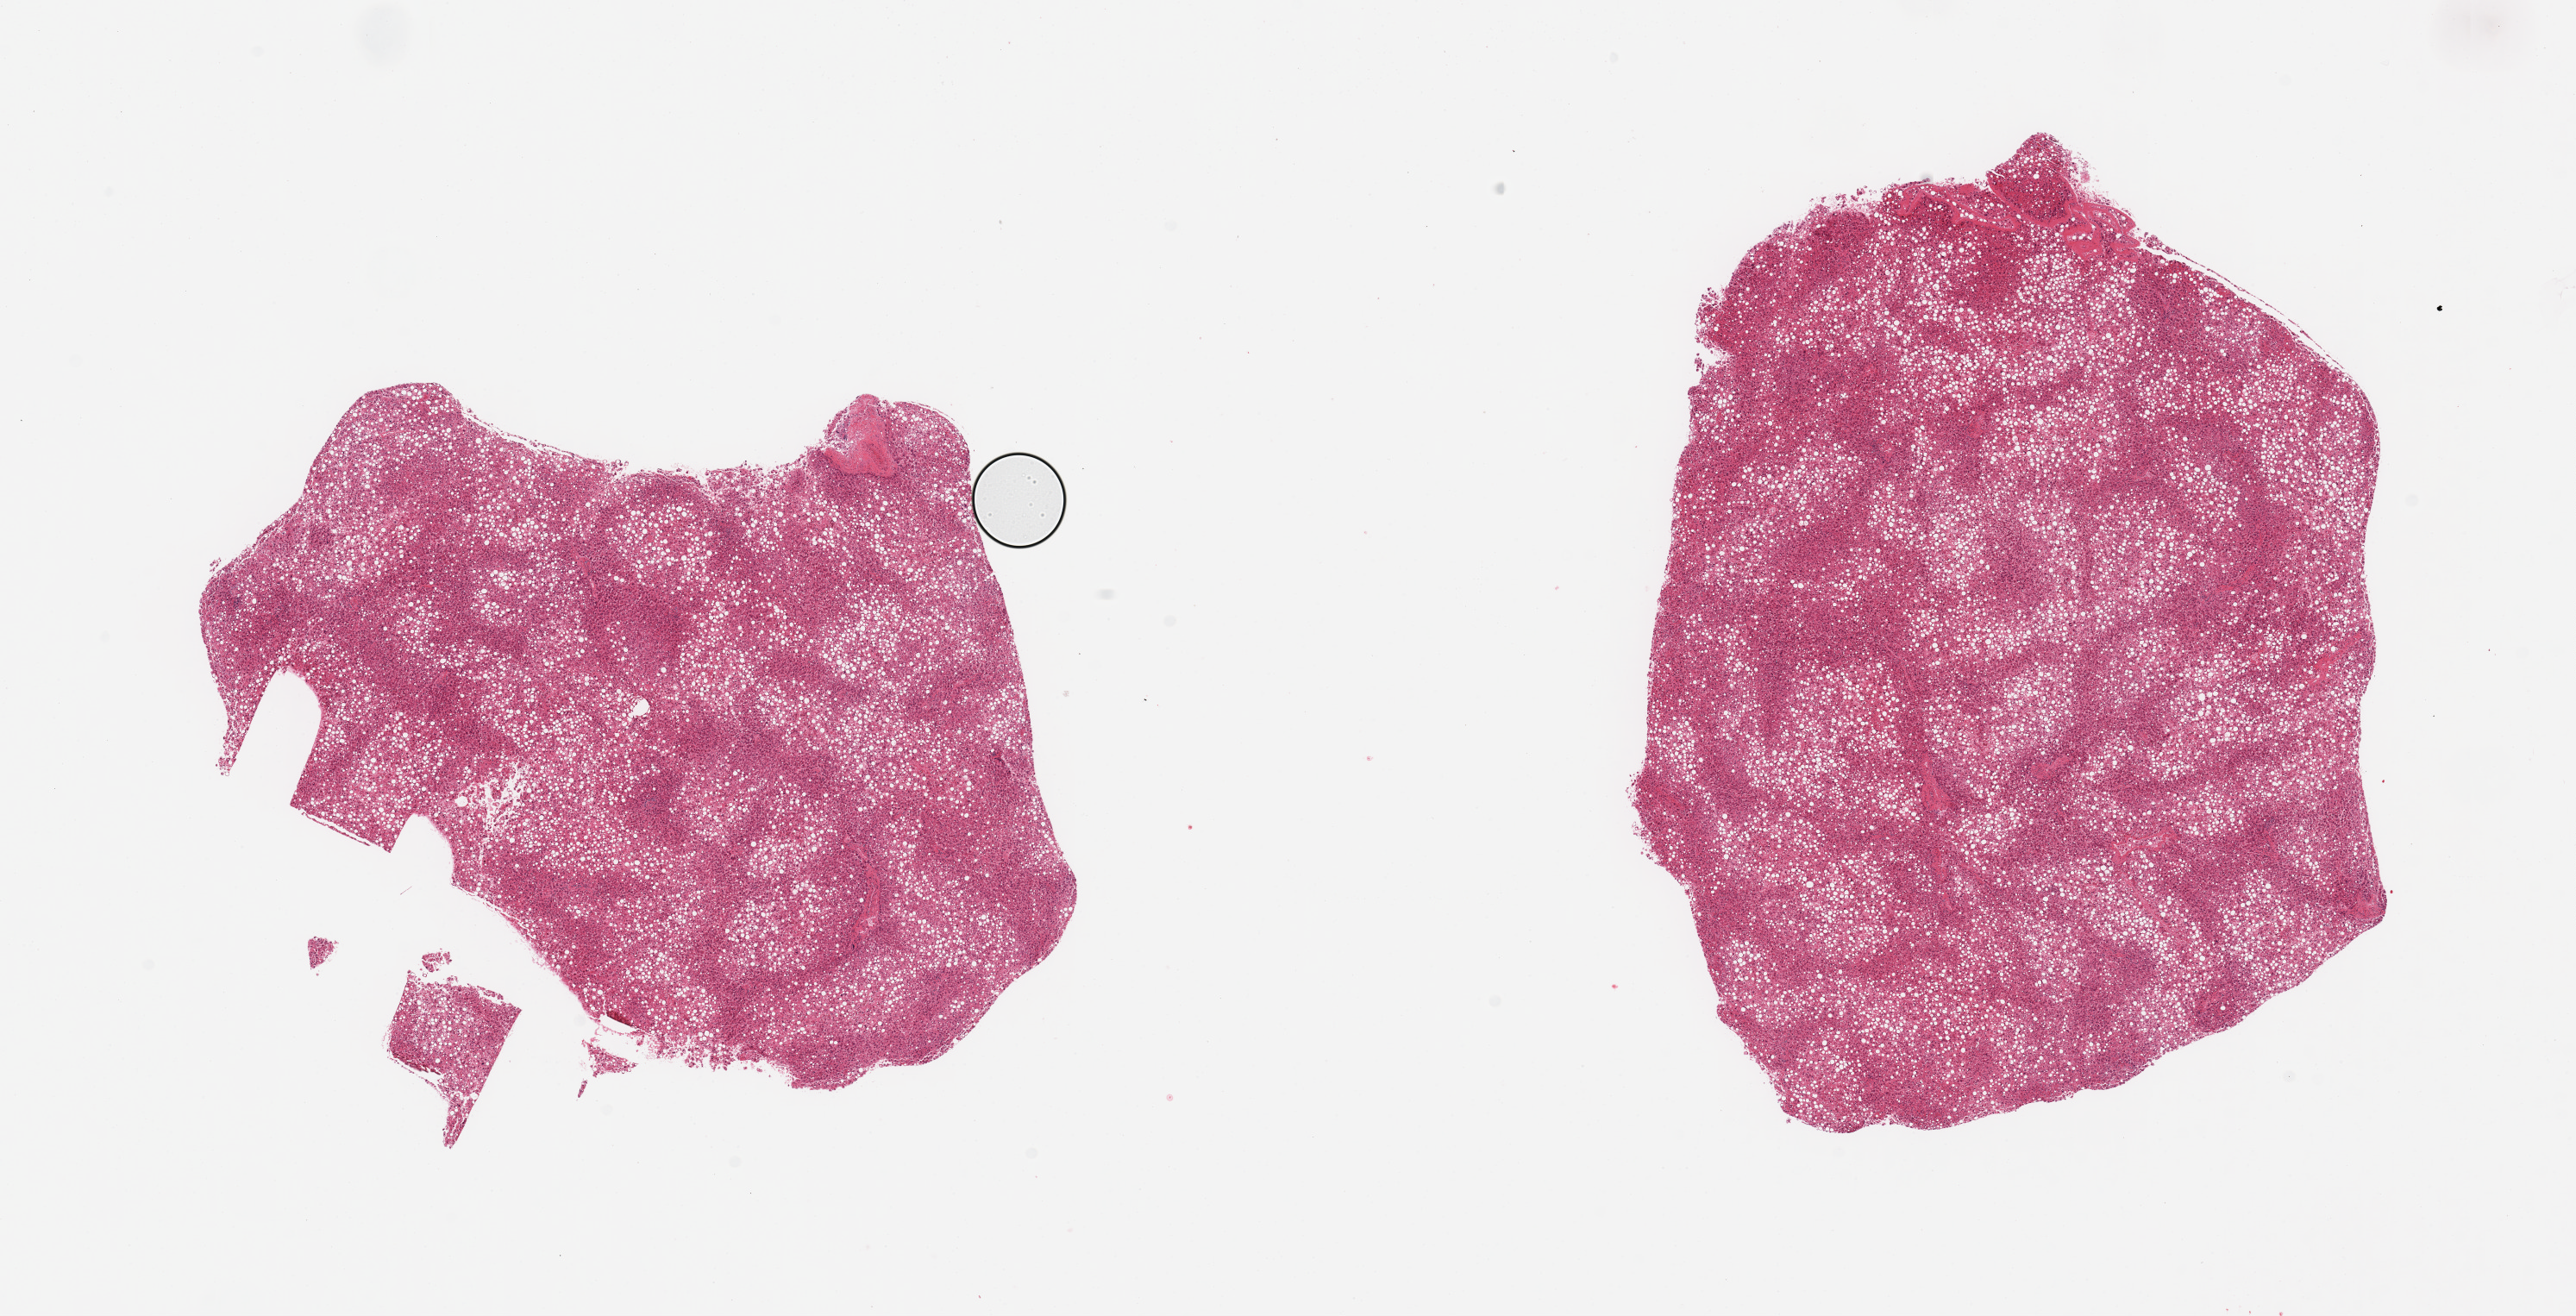
Digitized haematoxylin and eosin-stained section, brightfield, a low-resolution overview of the entire scanned area, about 23.6 x 12.1 mm (acquisition: 20x scan); PAXgene-fixed, paraffin-embedded tissue; sampled site (target tissue): liver; donor tissue sample. Donor sex: male.
Reviewer comment on this tissue sample: 2 pieces; marked steatosis and congestion.